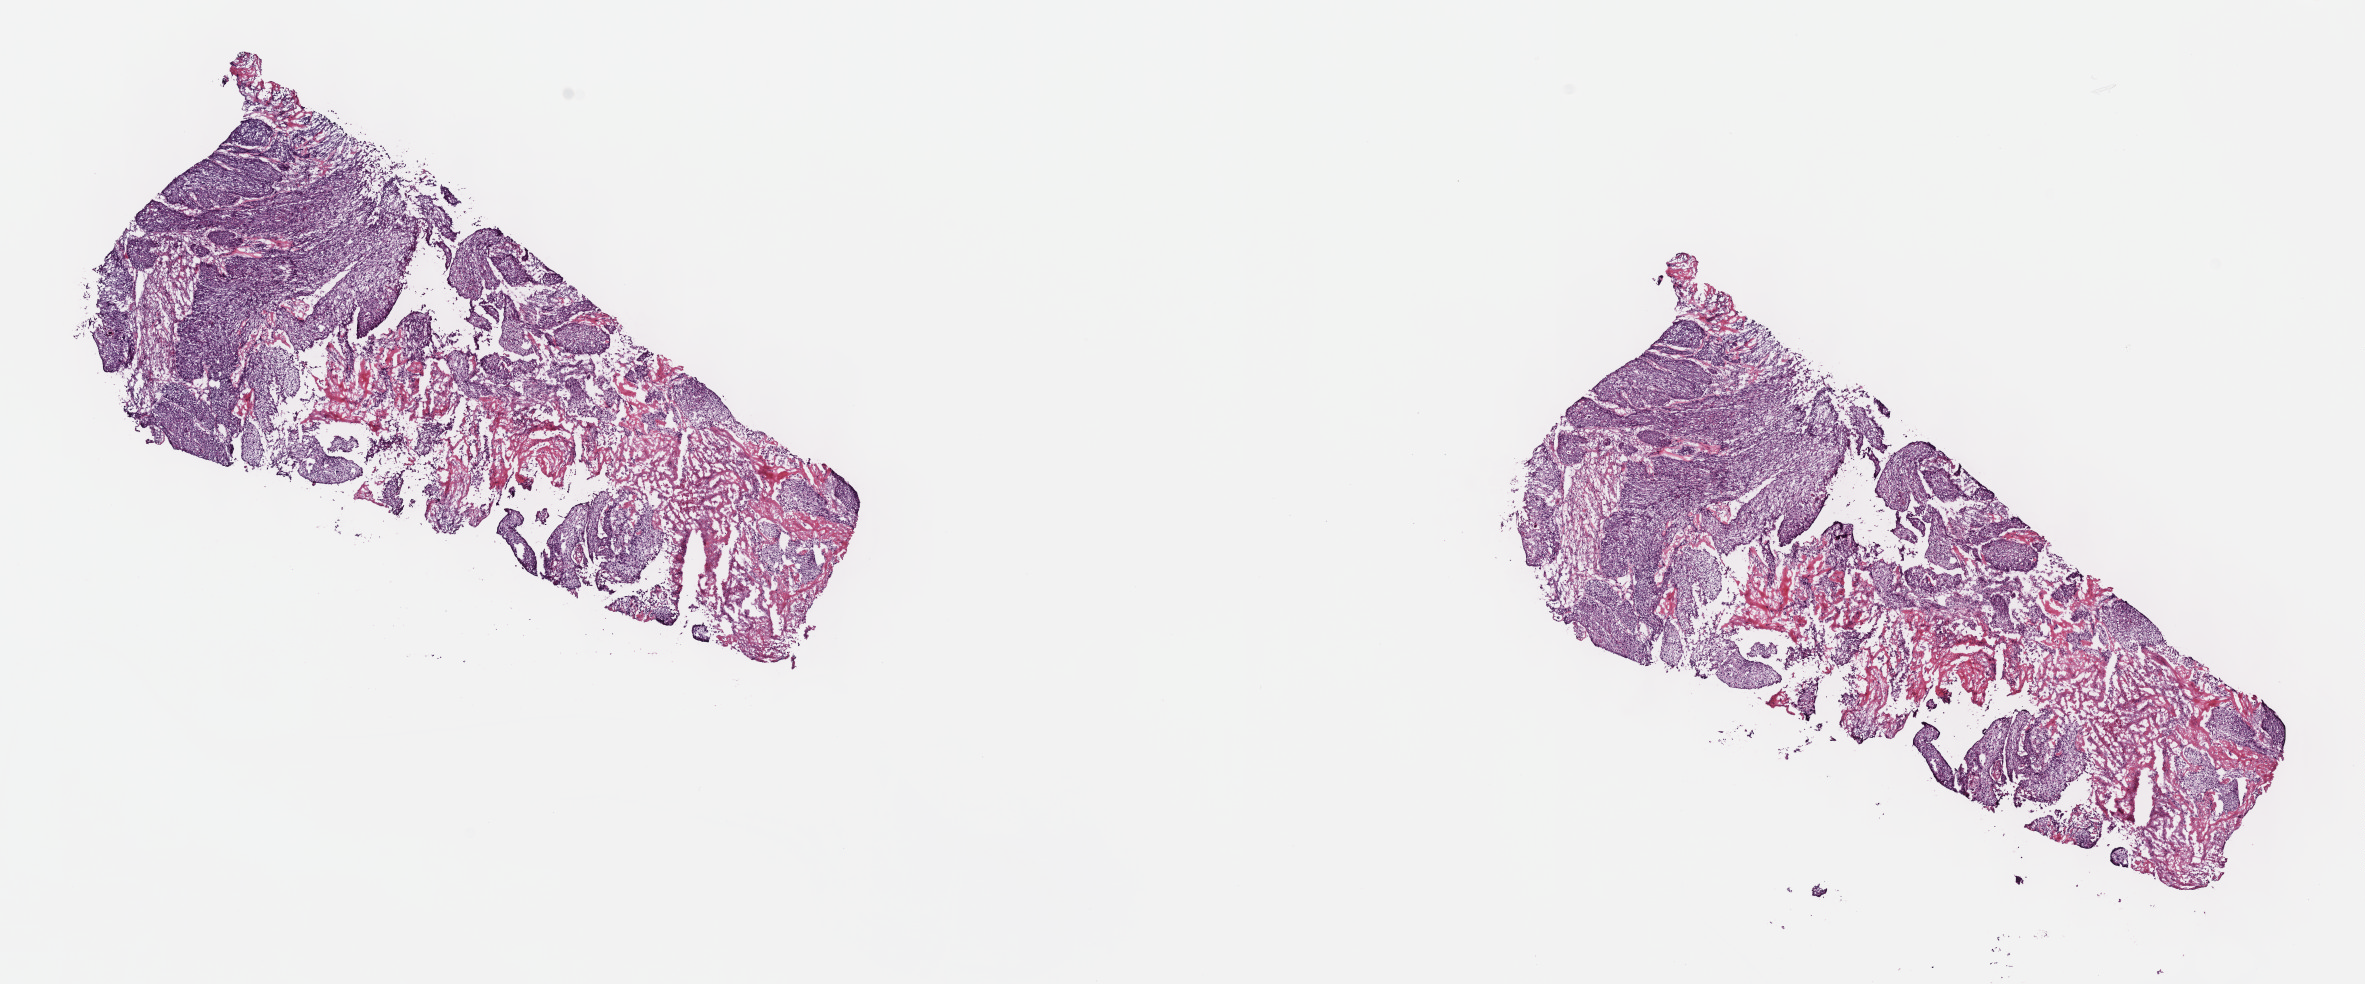
H&E whole-slide image — a low-resolution overview of the entire scanned area, about 19.1 x 8.0 mm (from a 40x scan). Frozen section from the top of the tissue portion. Sample: primary tumour, cervix. Patient: female, age at initial diagnosis 48 years. Histologic grade: G2 (moderately differentiated). Composition of this section per pathologist review: tumour cells 85%, tumour nuclei 75%, normal cells 0%, stromal cells 0%, necrosis 15%. Infiltration values recorded for this section: lymphocyte infiltration 5%, monocyte infiltration 0%, neutrophil infiltration 0%.
FIGO stage: IIIB. Histologic diagnosis: Squamous cell carcinoma, NOS.